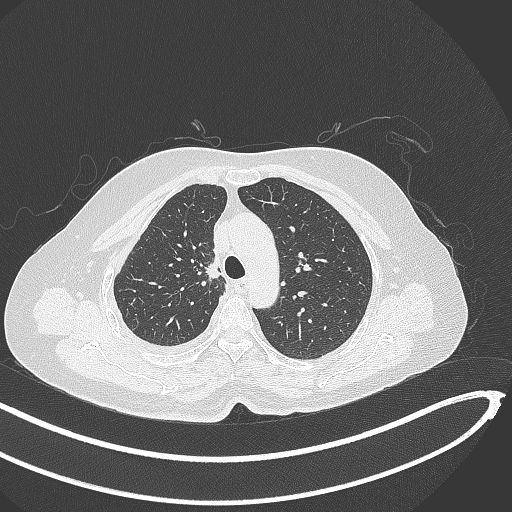
Chest CT, one axial slice. Position 277 of 345 along the scan axis. Reconstruction kernel B70f. 120 kVp. Lung window (W 1500 / L -600 HU). 512 × 512 image matrix, field of view 400 × 400 mm. Female patient, age 64 years. From the clinical record (not read from this slice): clinical TNM (as recorded): T1b N0 M1.
Structures marked on this image (bounding box drawn by a radiologist):
- lung tumour (recorded histology: adenocarcinoma): bounding box <201,257,226,286> (left, top, right, bottom; pixels)